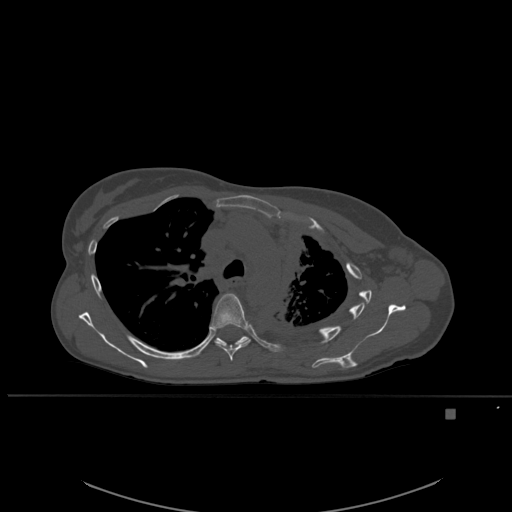
CT including the spine, one axial slice. Slice 394 of 537 in the series (ordered by position). Bone window (W 1800 / L 400 HU). 1.5 mm slice thickness. 512 × 512 image matrix. Patient: female, 45 years. From the clinical record (not read from this slice): primary cancer: lung.
Outlined on this slice (semi-automatic segmentation, software-assisted and operator-edited):
- T5 vertebra: bounding box (x1, y1, x2, y2) in pixels: (210, 293, 251, 361)
- T6 vertebra: (214, 336, 249, 346)